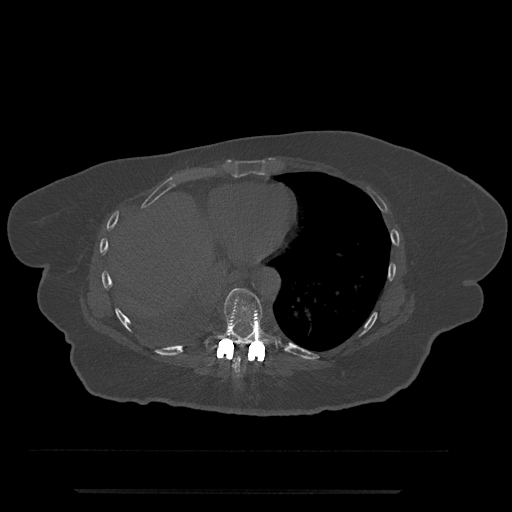
CT including the spine, one axial slice; slice 346 of 797 in the series (ordered by position); reconstruction kernel Br40s/3; 120 kVp; bone window (W 1800 / L 400 HU); 0.5 mm slice thickness; 512 × 512 image matrix, field of view 440 × 440 mm. Female patient, age 51 years. Case-level facts recorded for this patient, not image findings: primary cancer: neuro.
Annotated regions visible in this slice (semi-automatic segmentation, software-assisted and operator-edited):
- T8 vertebra: bounding box <233,346,250,375> (left, top, right, bottom; pixels)
- T9 vertebra: <205,288,277,353>